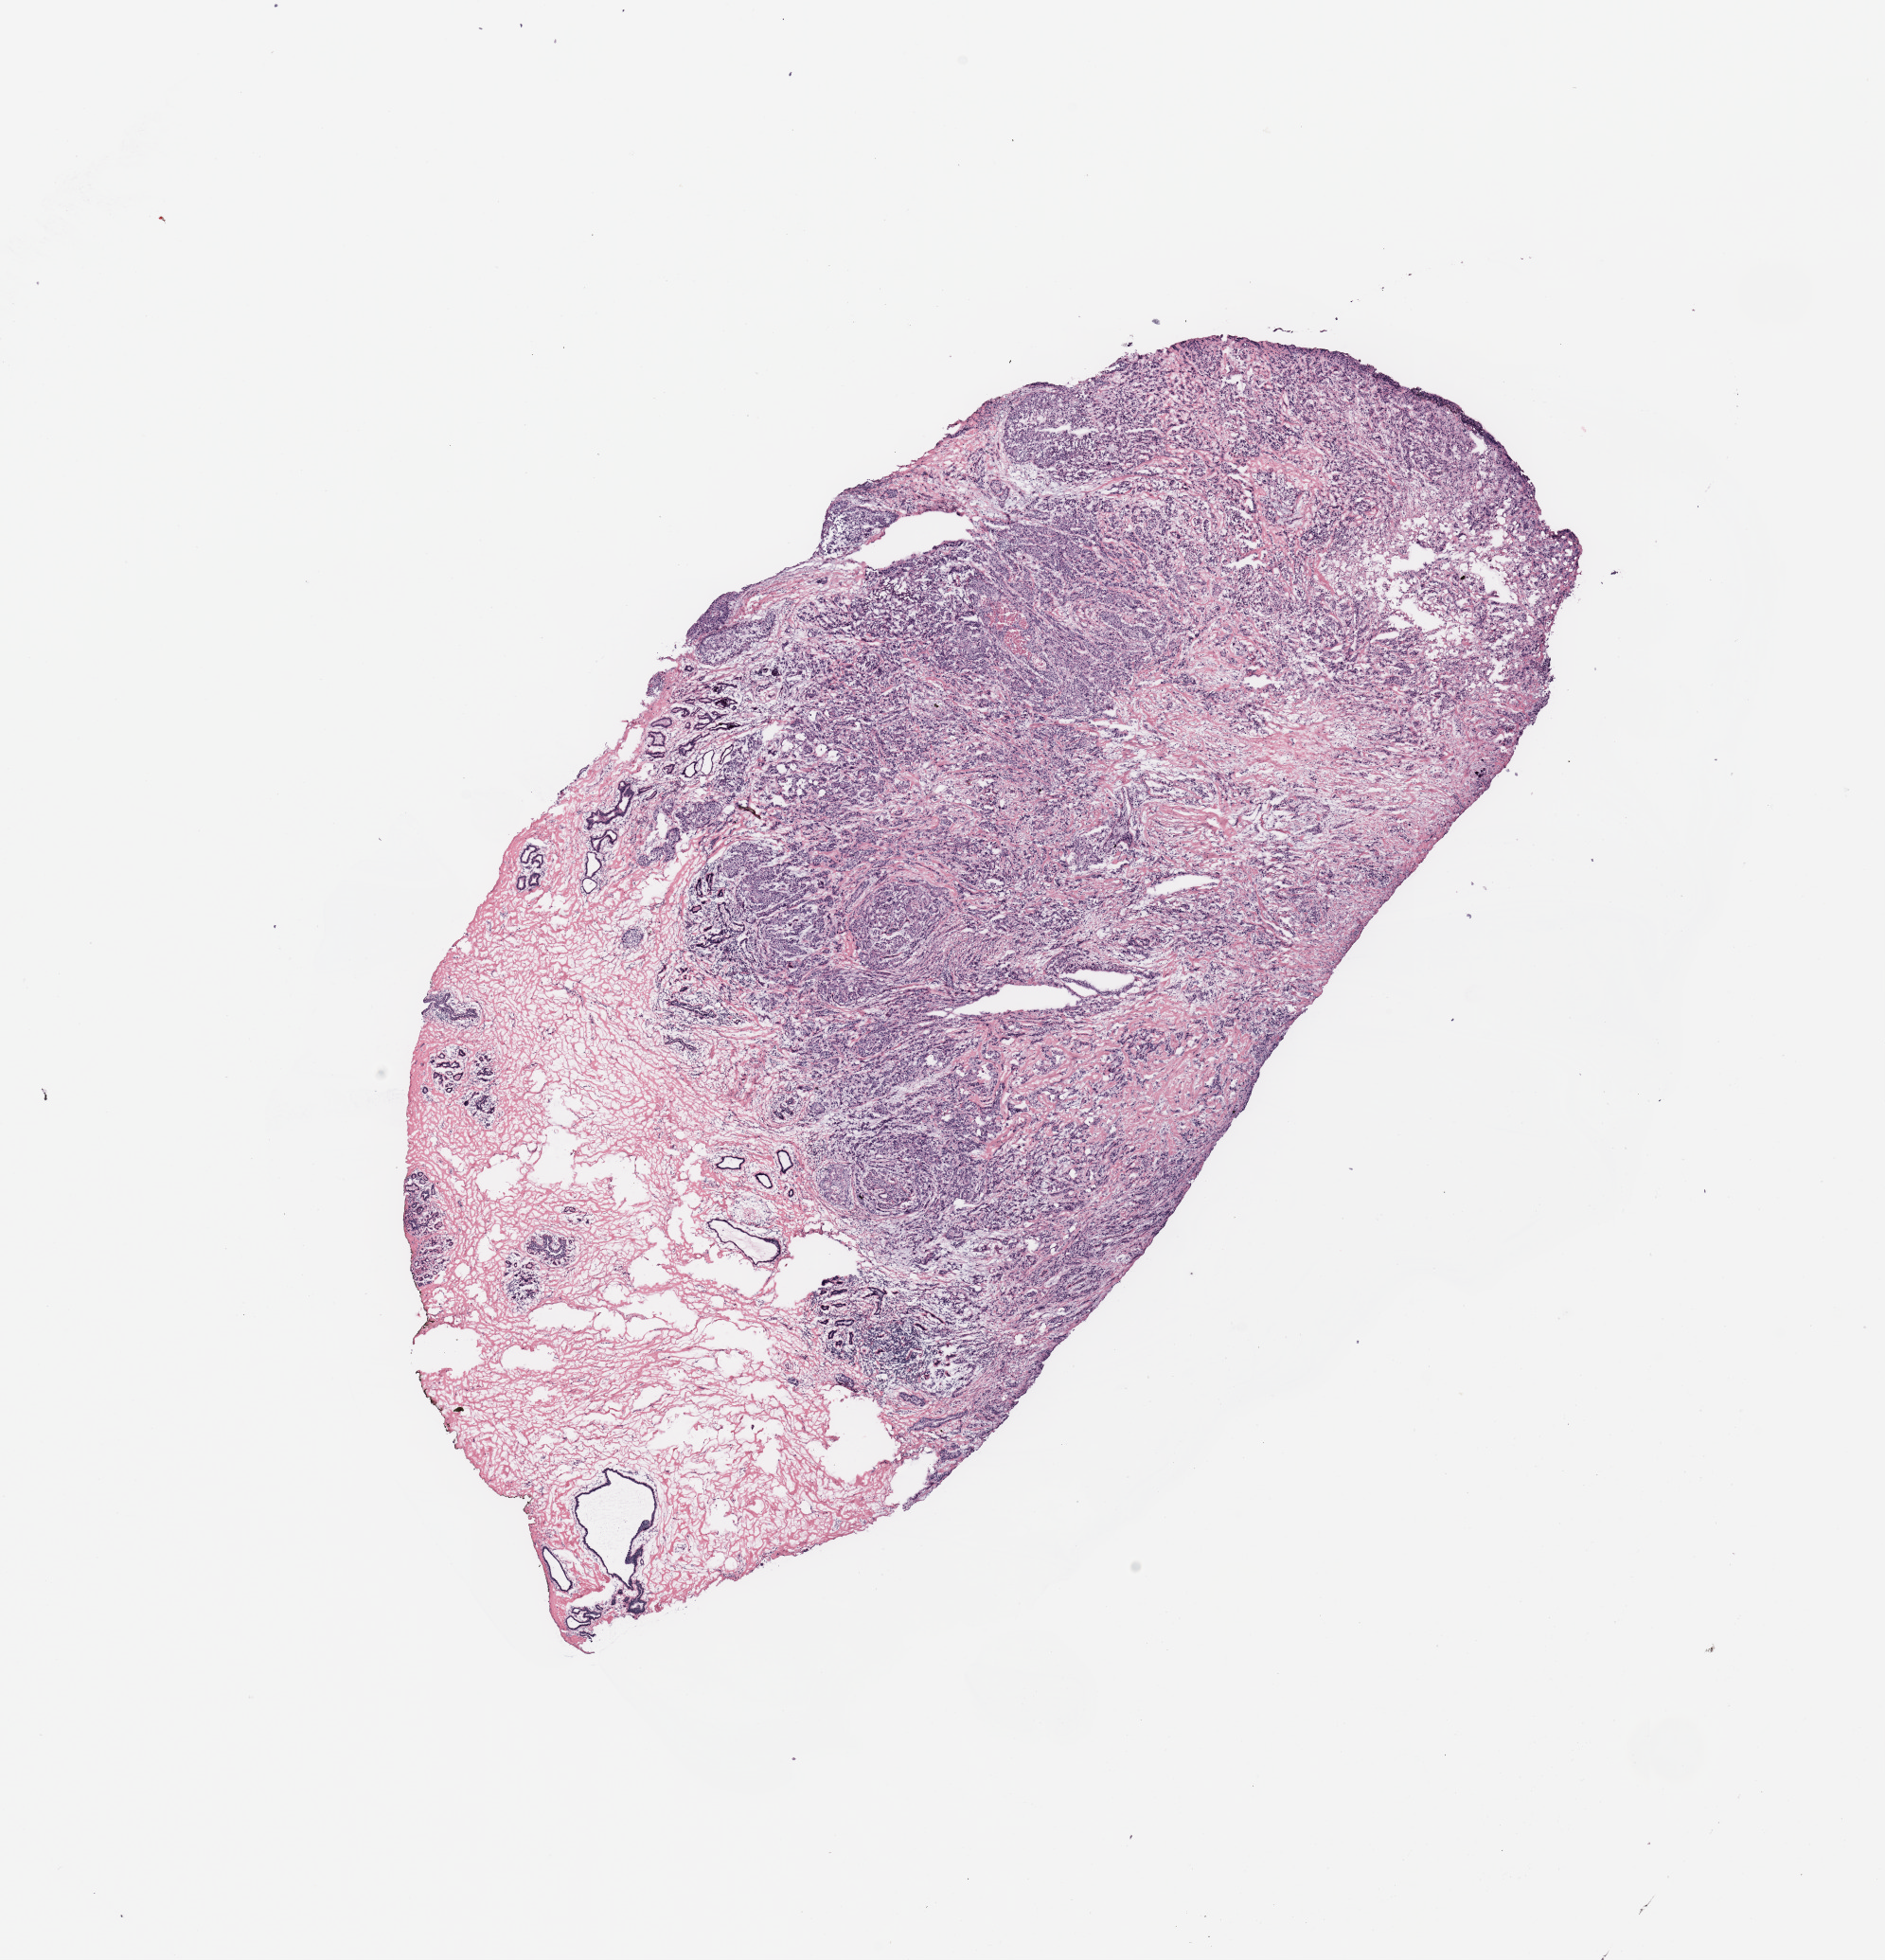
Hematoxylin and eosin (H&E) stained whole-slide image, shown as a low-resolution overview of the whole scanned area (about 15.8 x 16.4 mm, from a 20x scan); breast, tumour tissue. Patient: female, age 46 years.
- histologic diagnosis: Infiltrating duct and lobular carcinoma
- AJCC pathologic stage: IIB